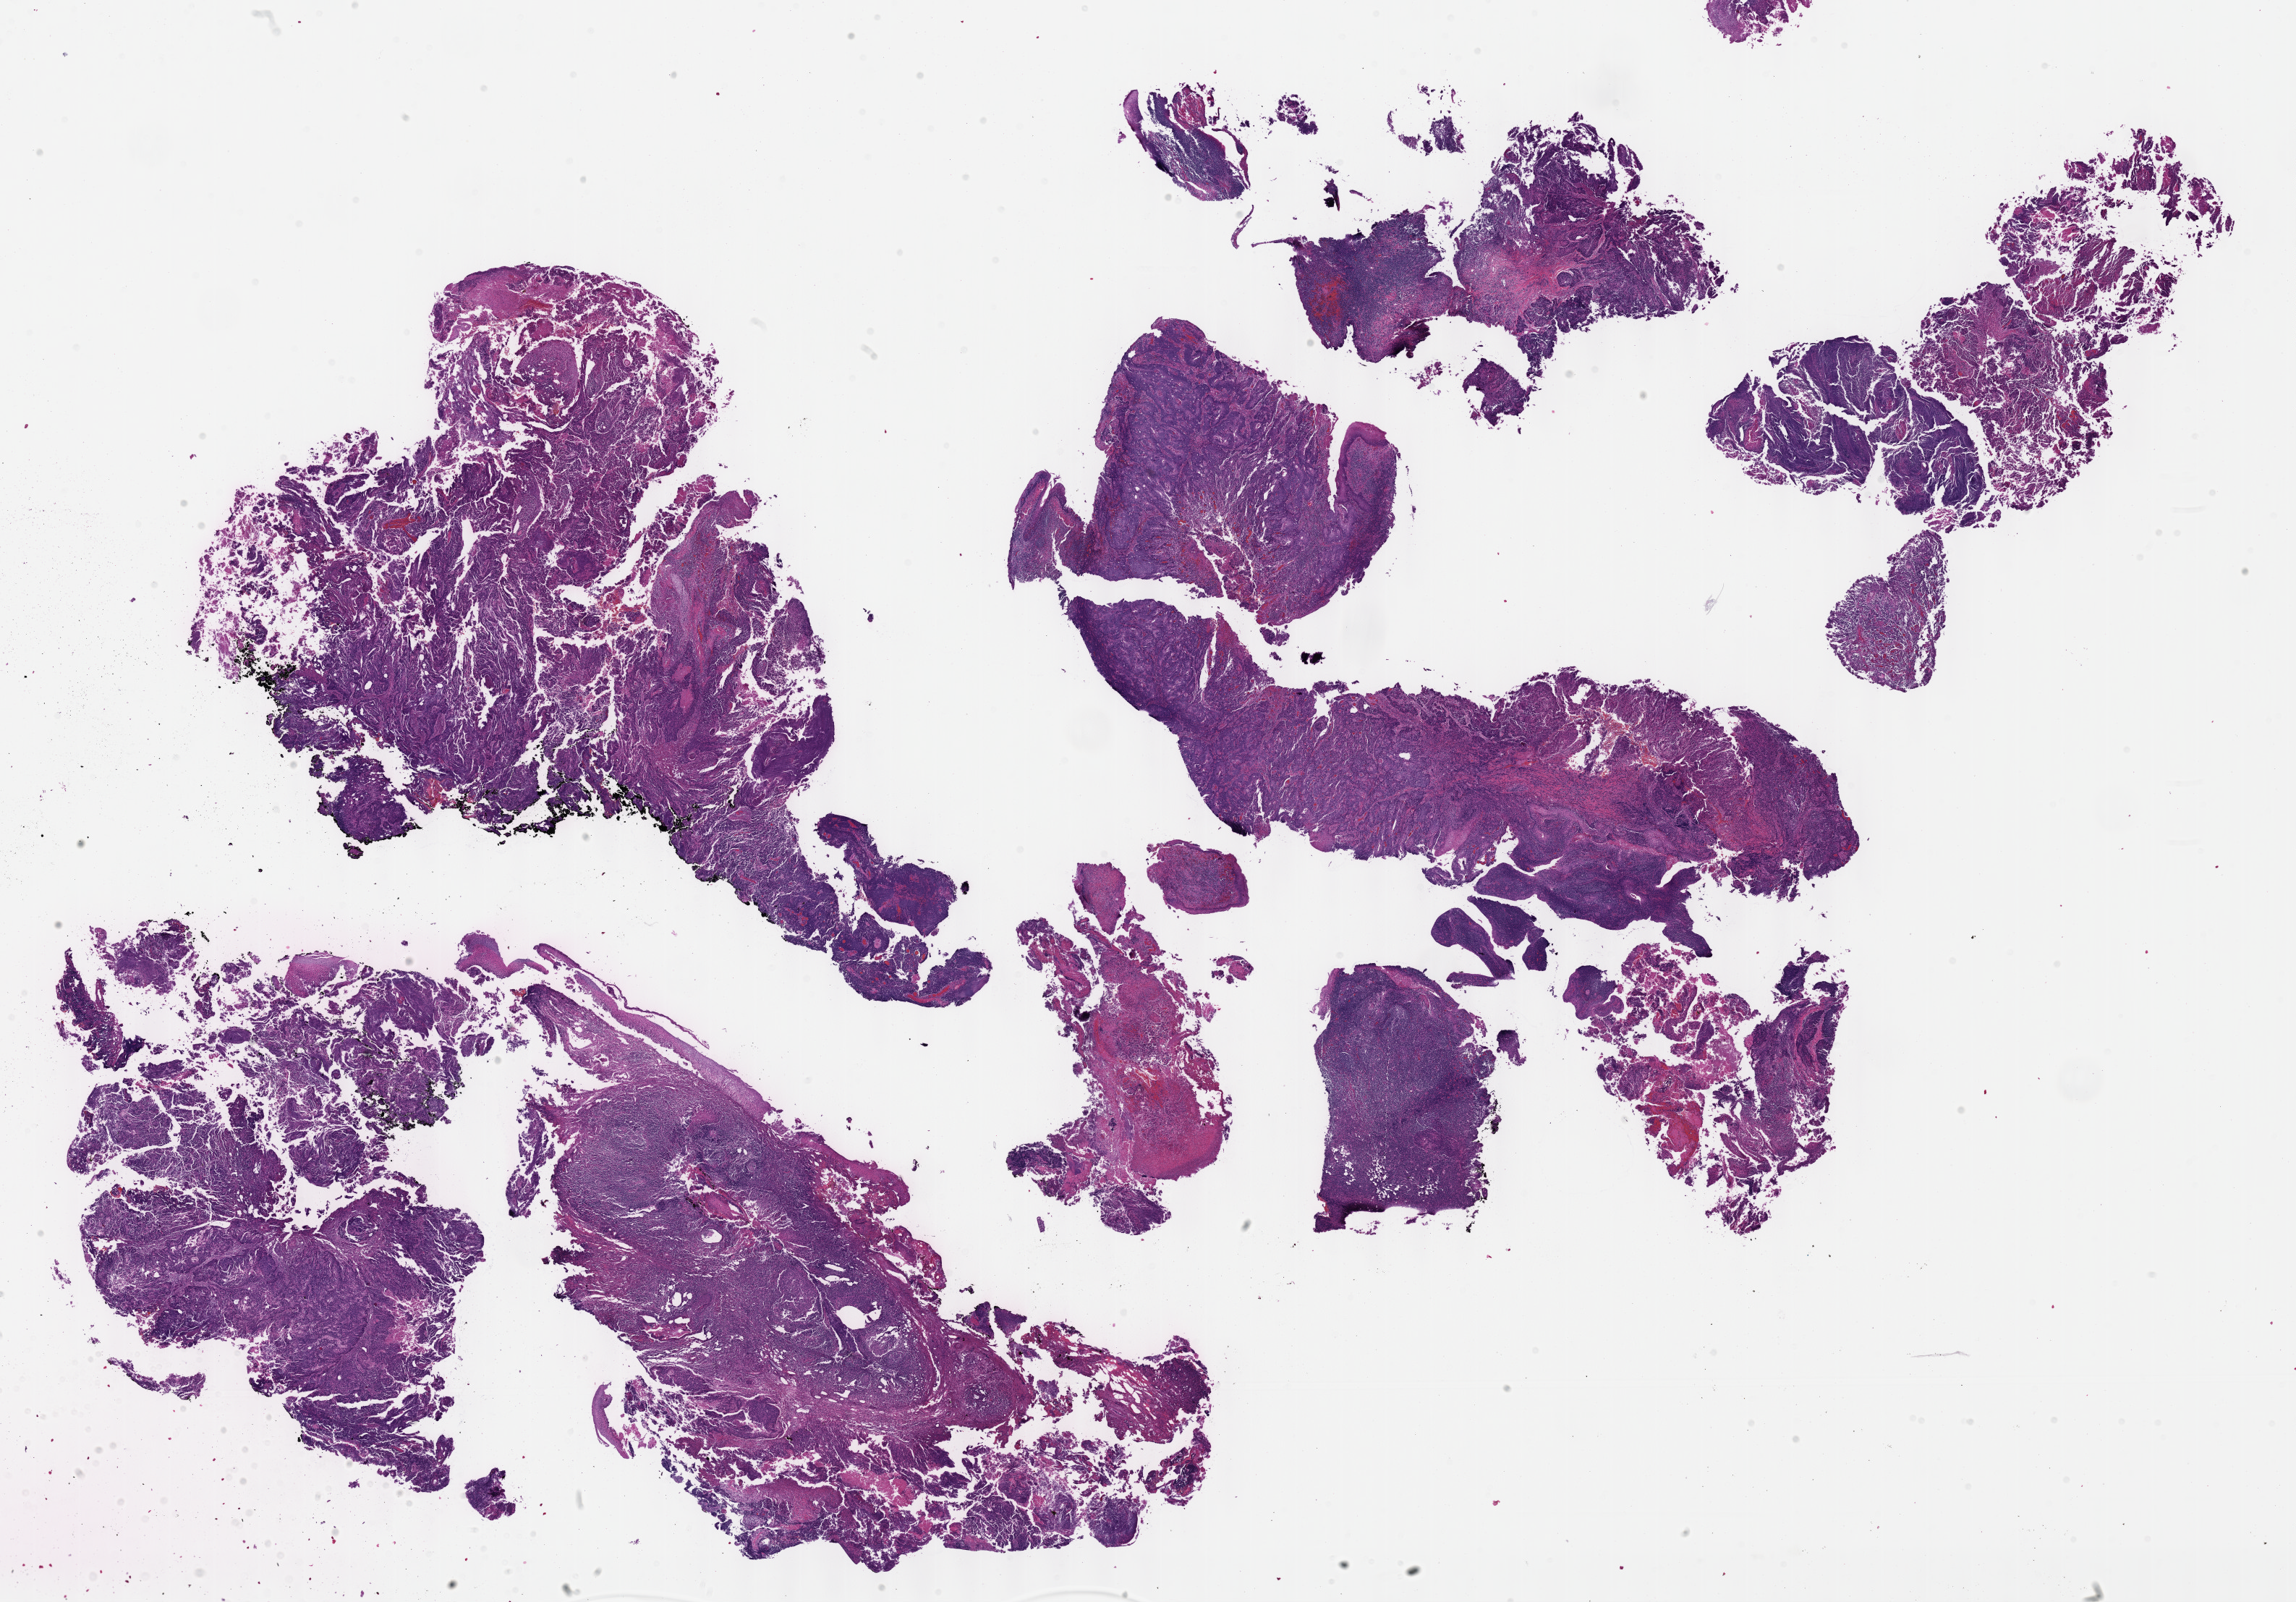
Hematoxylin and eosin (H&E) stained whole-slide image — a low-resolution overview of the entire scanned area, about 25.7 x 17.9 mm, formalin-fixed paraffin-embedded (FFPE) diagnostic section, head and neck, primary tumour sample. Patient: male, age at initial diagnosis 40 years. Histologic grade: GX (grade cannot be assessed).
* laterality: right
* diagnosis: Squamous cell carcinoma, NOS (tonsil, NOS)